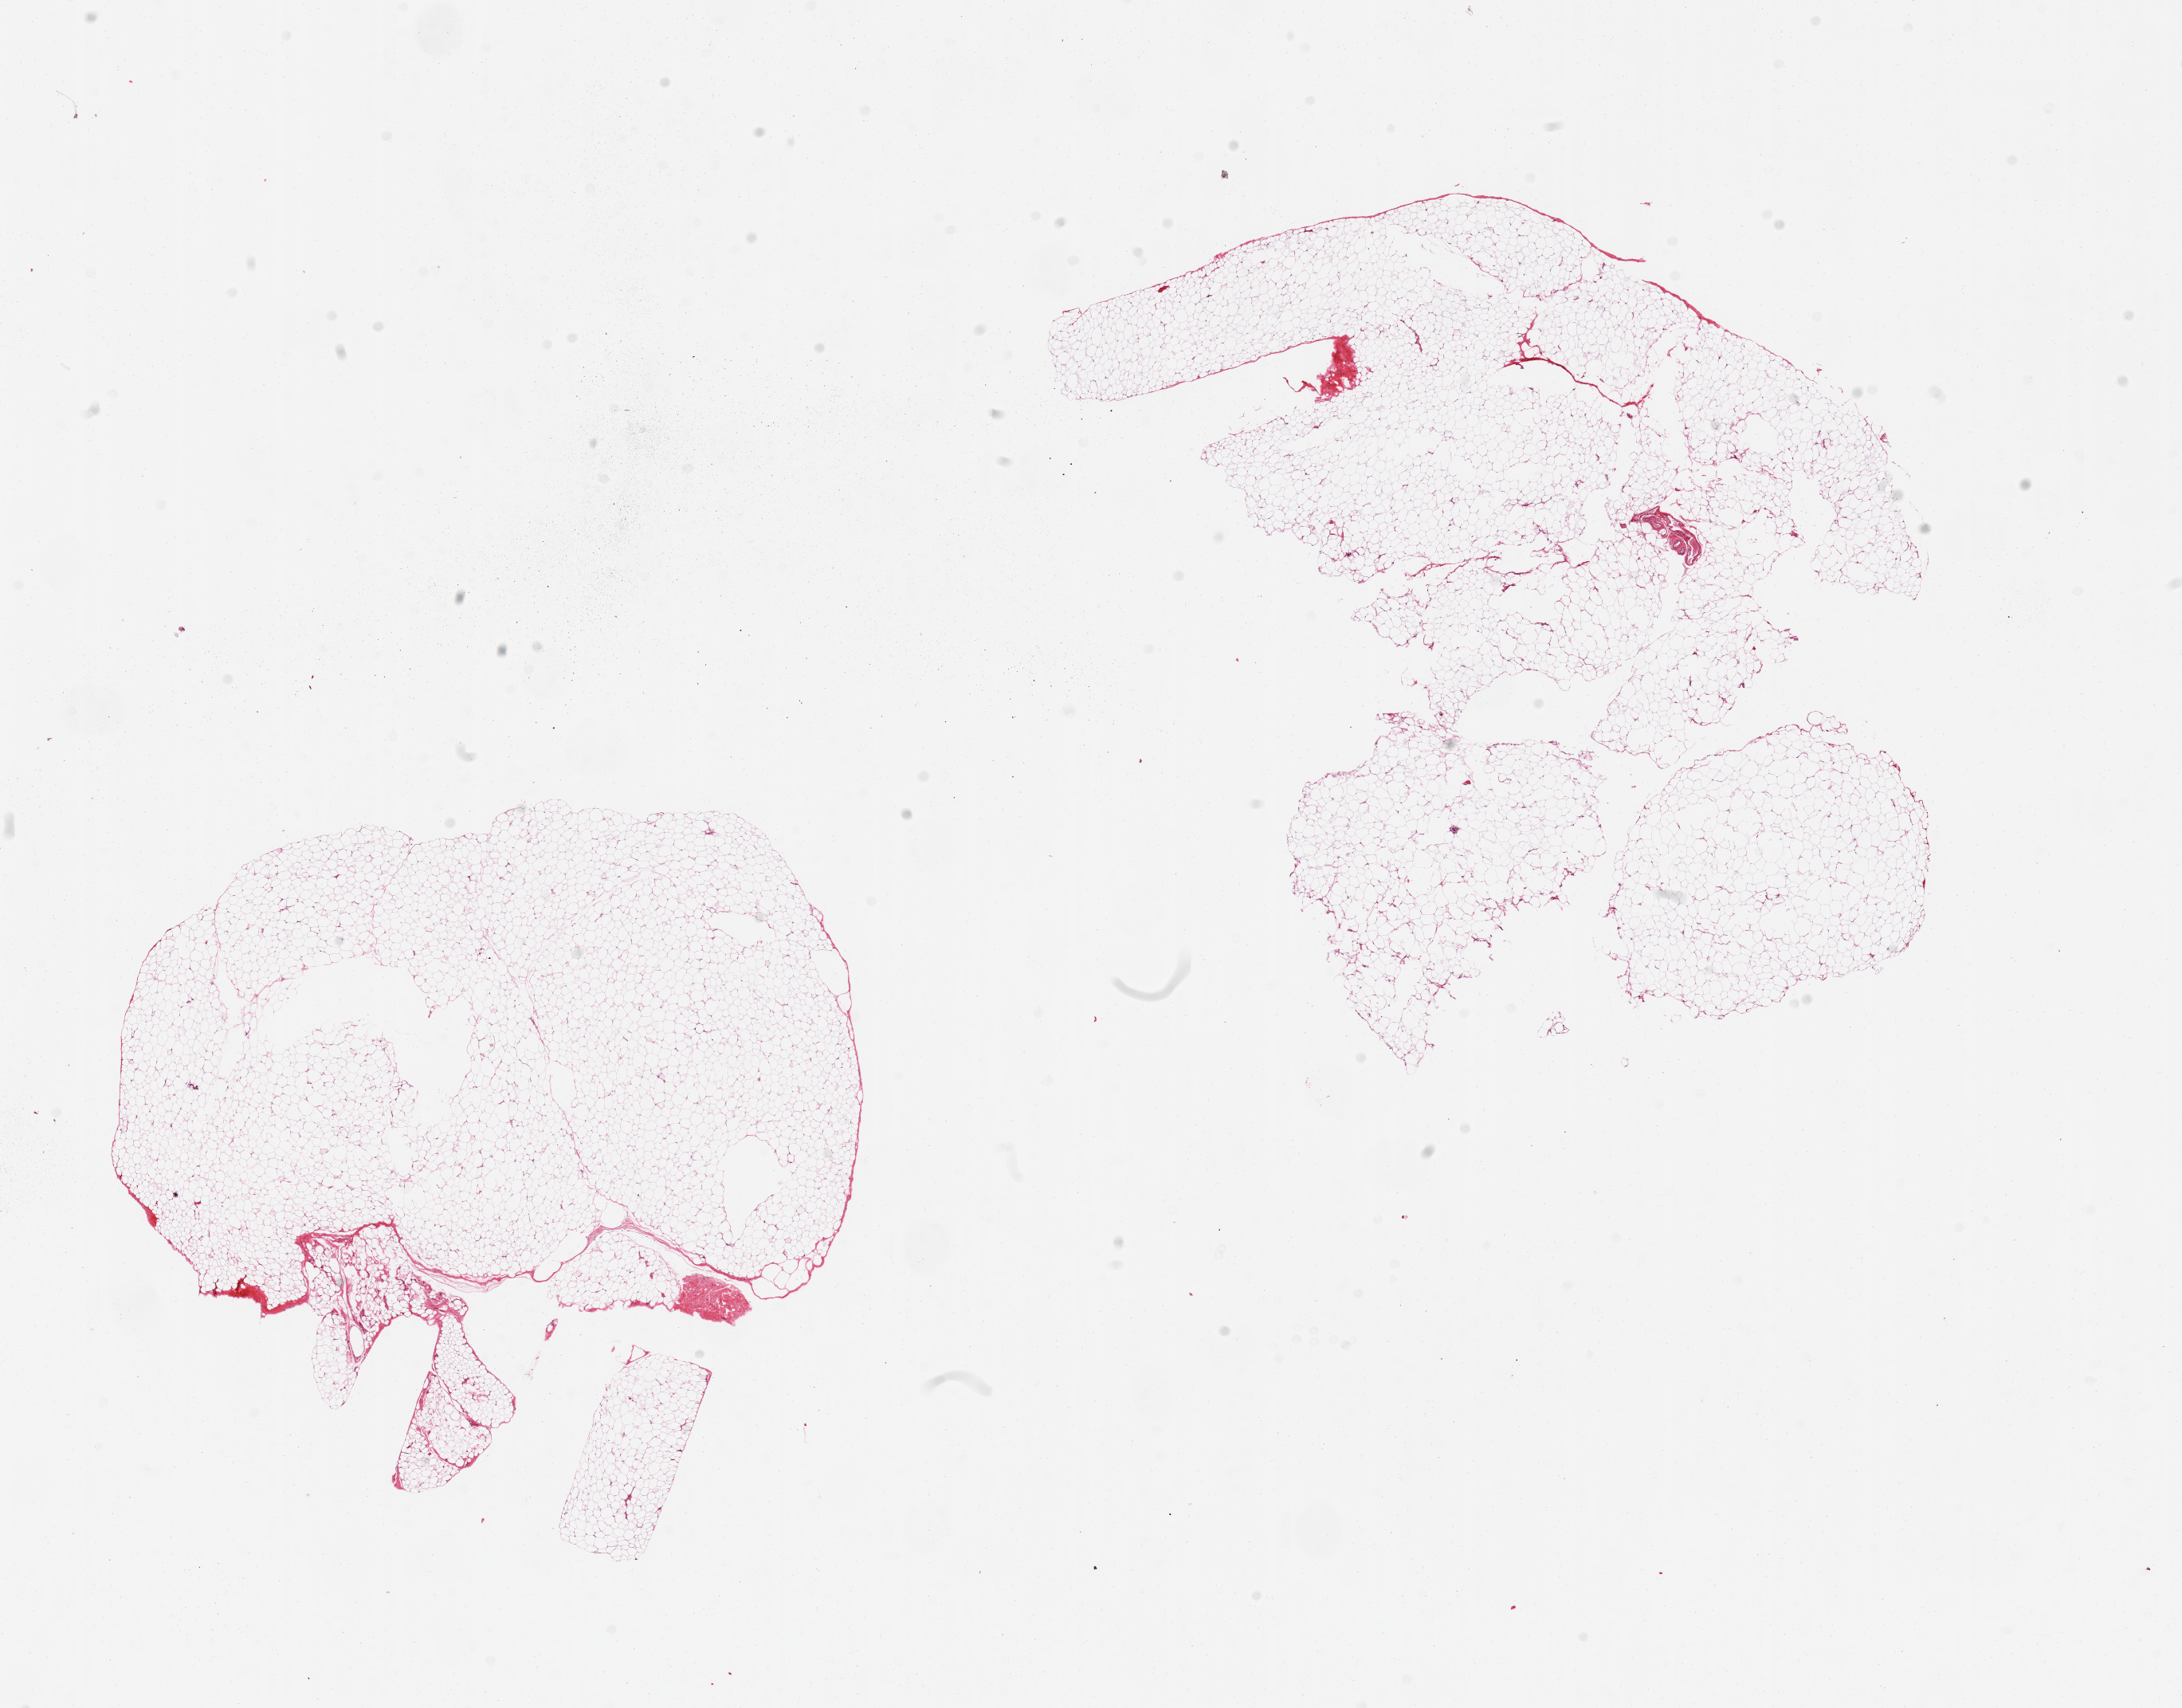
Hematoxylin and eosin (H&E) whole-slide image, brightfield — low-resolution overview of the scanned area, about 21.7 x 17.0 mm (acquisition: 20x scan). PAXgene-fixed, paraffin-embedded tissue. Section of breast (target tissue). Donor tissue sample. Donor sex: male.
- pathologist's review note for this sample: 2 pieces, predominantly fat, scant stroma and vessels